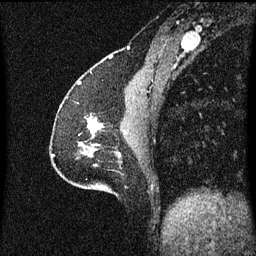
Breast MRI (dynamic contrast-enhanced), one sagittal slice; position 22 of 60 along the scan axis; dynamic contrast-enhanced series, image 2 of 3 at this slice position (ordered by acquisition); 1.5 T; TE 4.2 ms, TR 8.4 ms; 2 mm slice thickness; 256 × 256 image matrix, field of view 200 × 200 mm. Patient: female, 51 years.
Structures marked on this image (semi-automatic segmentation, software-assisted and operator-edited):
- analysis volume of interest (the breast-tissue region the enhancement analysis was run in; not a lesion): box from (x=85, y=114) to (x=104, y=139) px
- tumour enhancement mask (voxels above the 70 % enhancement threshold inside the analysis volume of interest): (x=88, y=118)–(x=103, y=133)